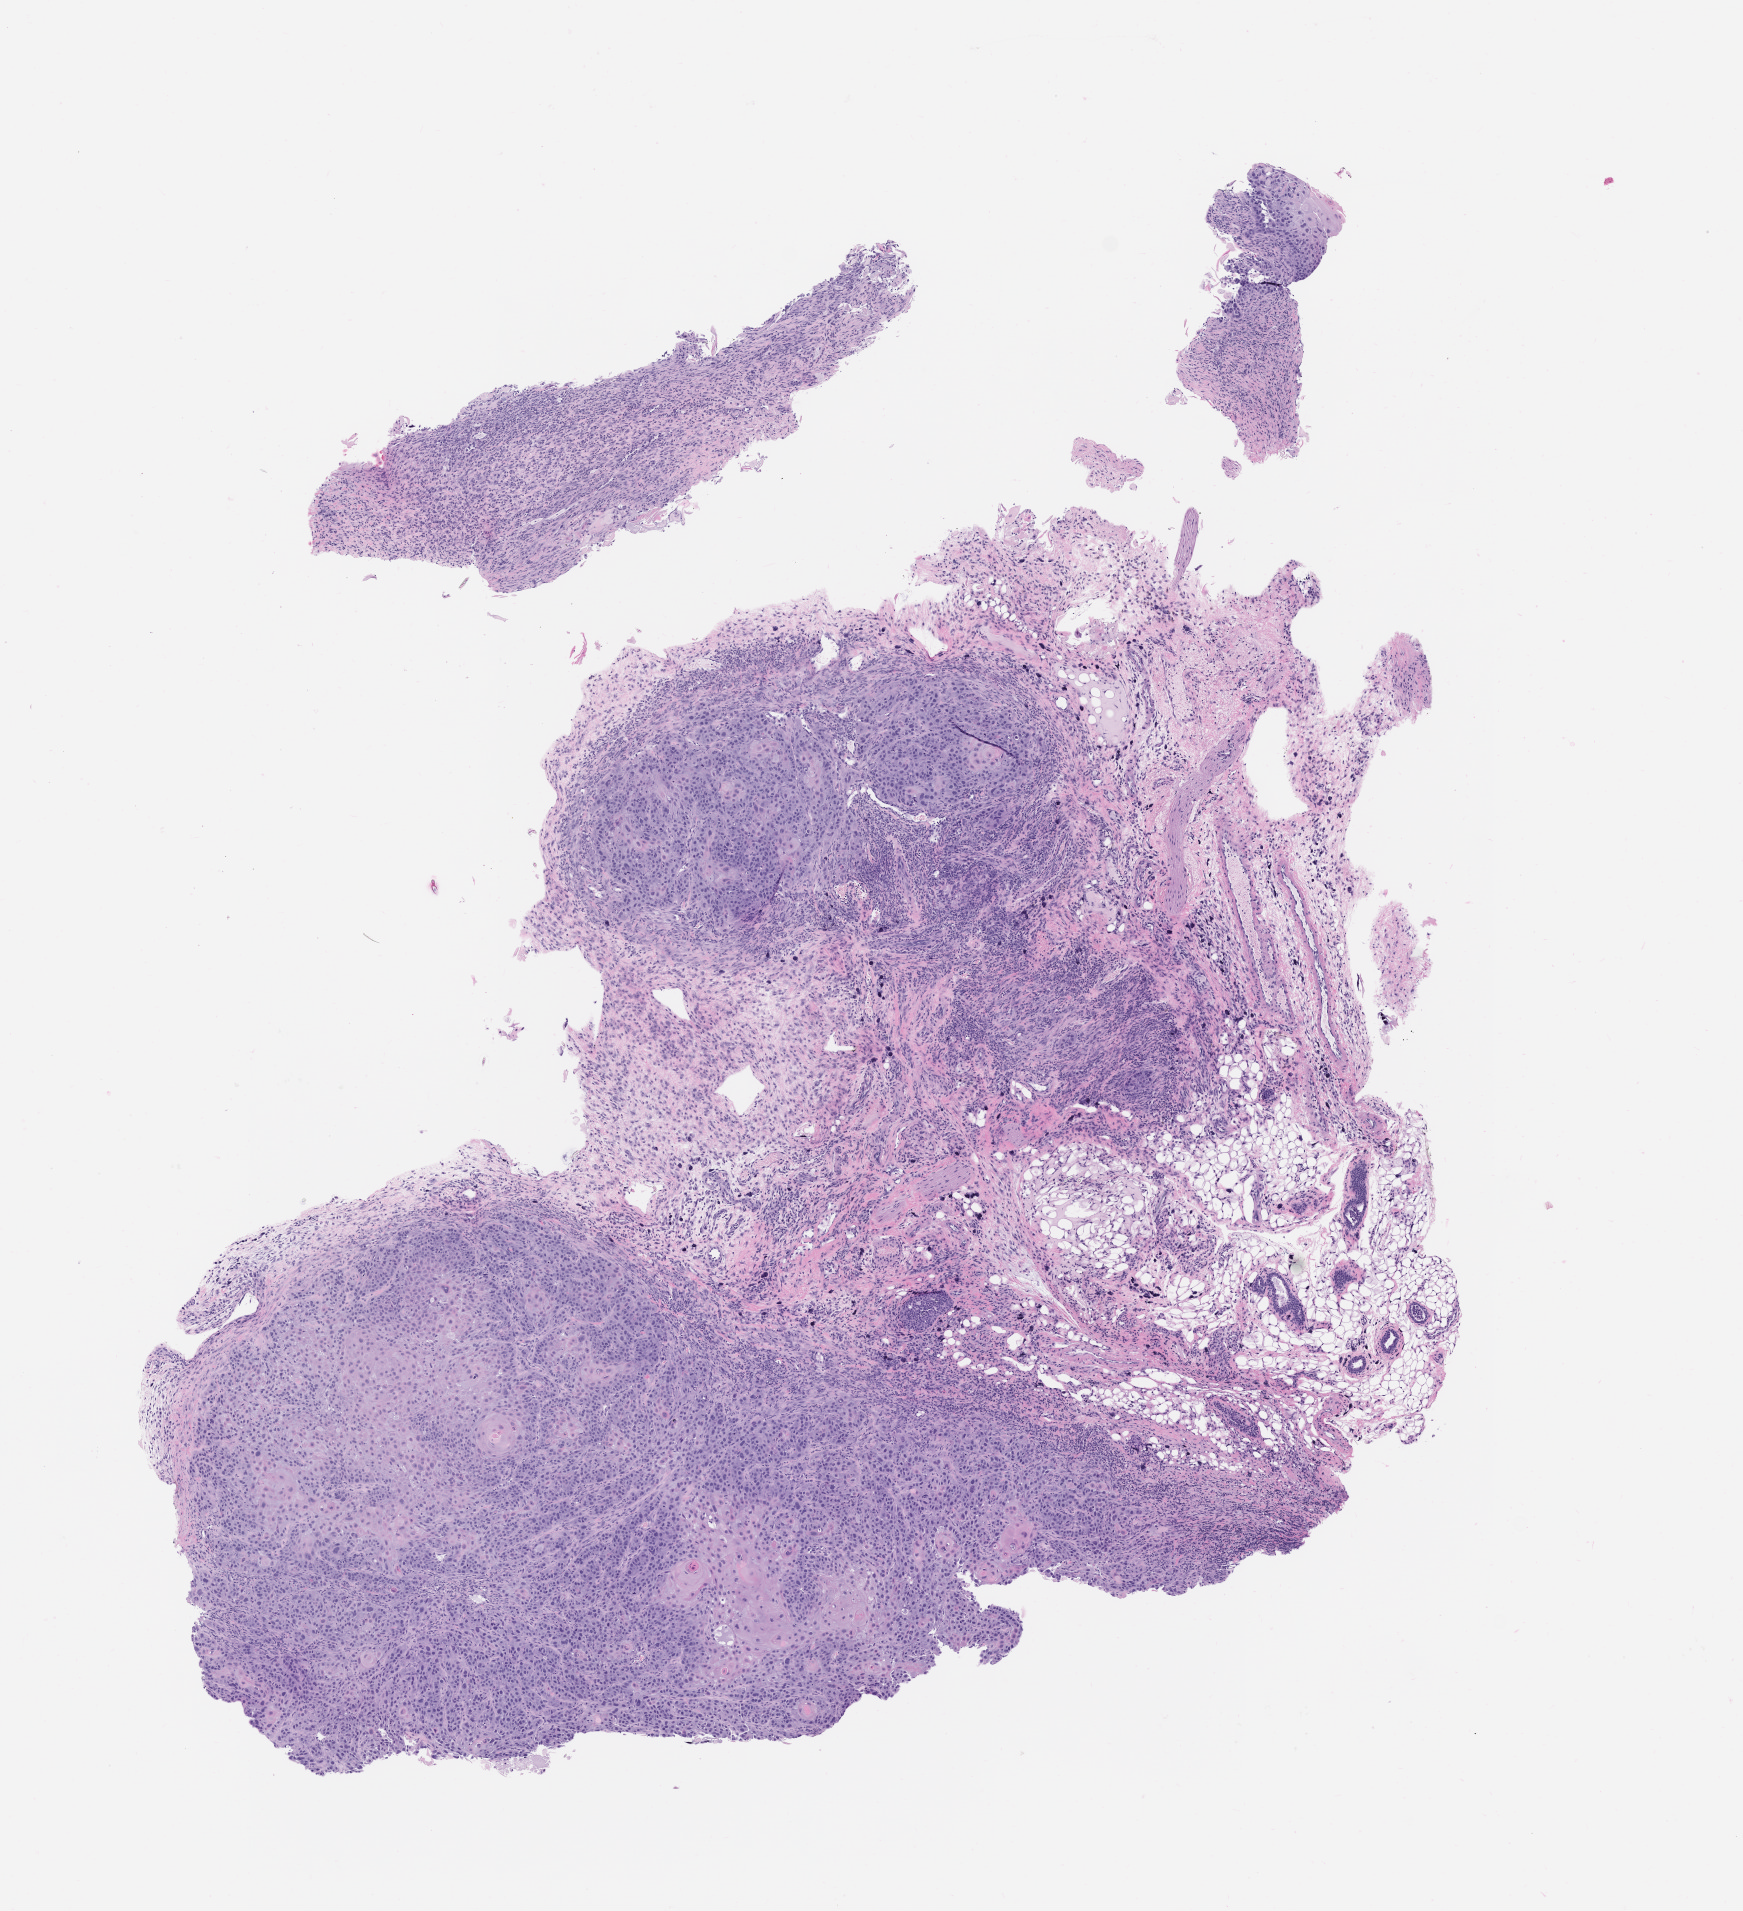
H&E whole-slide image of a patient-derived xenograft (PDX) tumor grown in a mouse, passage 2 — shown as a low-resolution overview of the whole scanned area (about 7.0 x 7.7 mm). Formalin-fixed, paraffin-embedded (FFPE) tissue. Originating tumor site category: oral soft tissue.
Originating patient diagnosis: Head and Neck Squamous Cell Carcinoma.